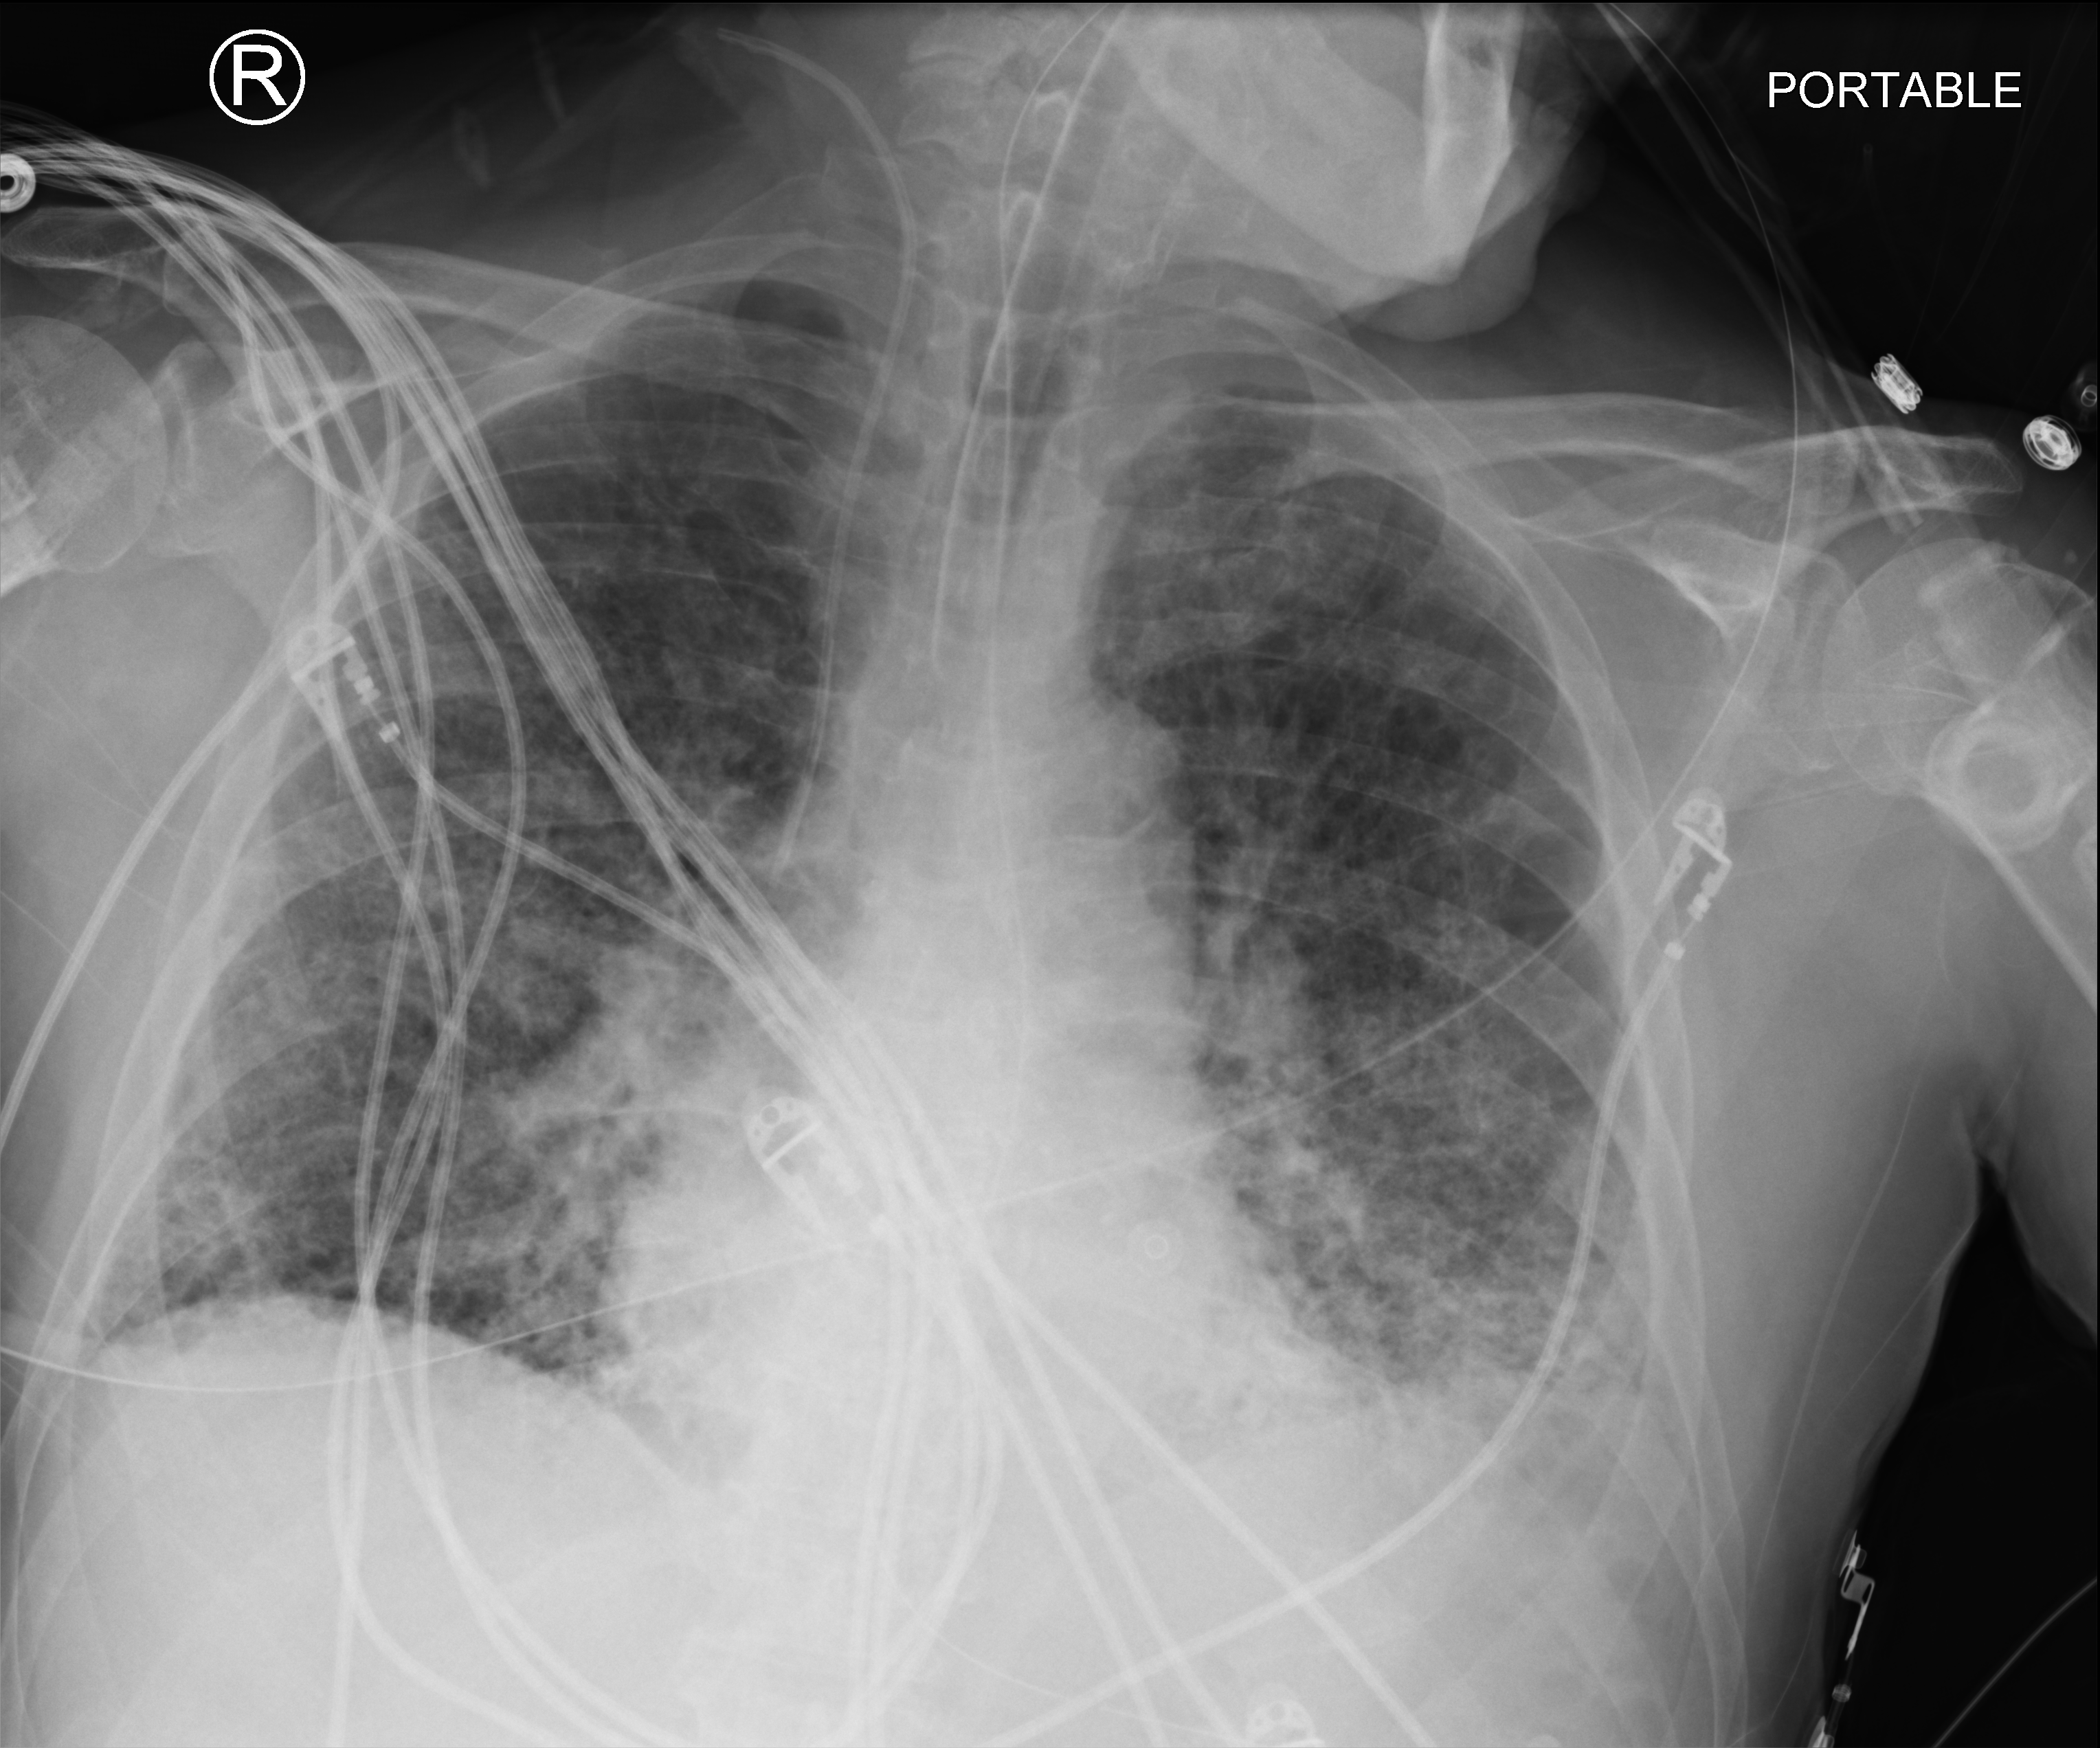
Portable chest radiograph; anteroposterior (AP) projection. Patient hospitalised with COVID-19; male, aged 75–90 years.
Admission-level facts for this patient (not findings on this image; timing relative to this image not recorded): smoking status (admission record): never.